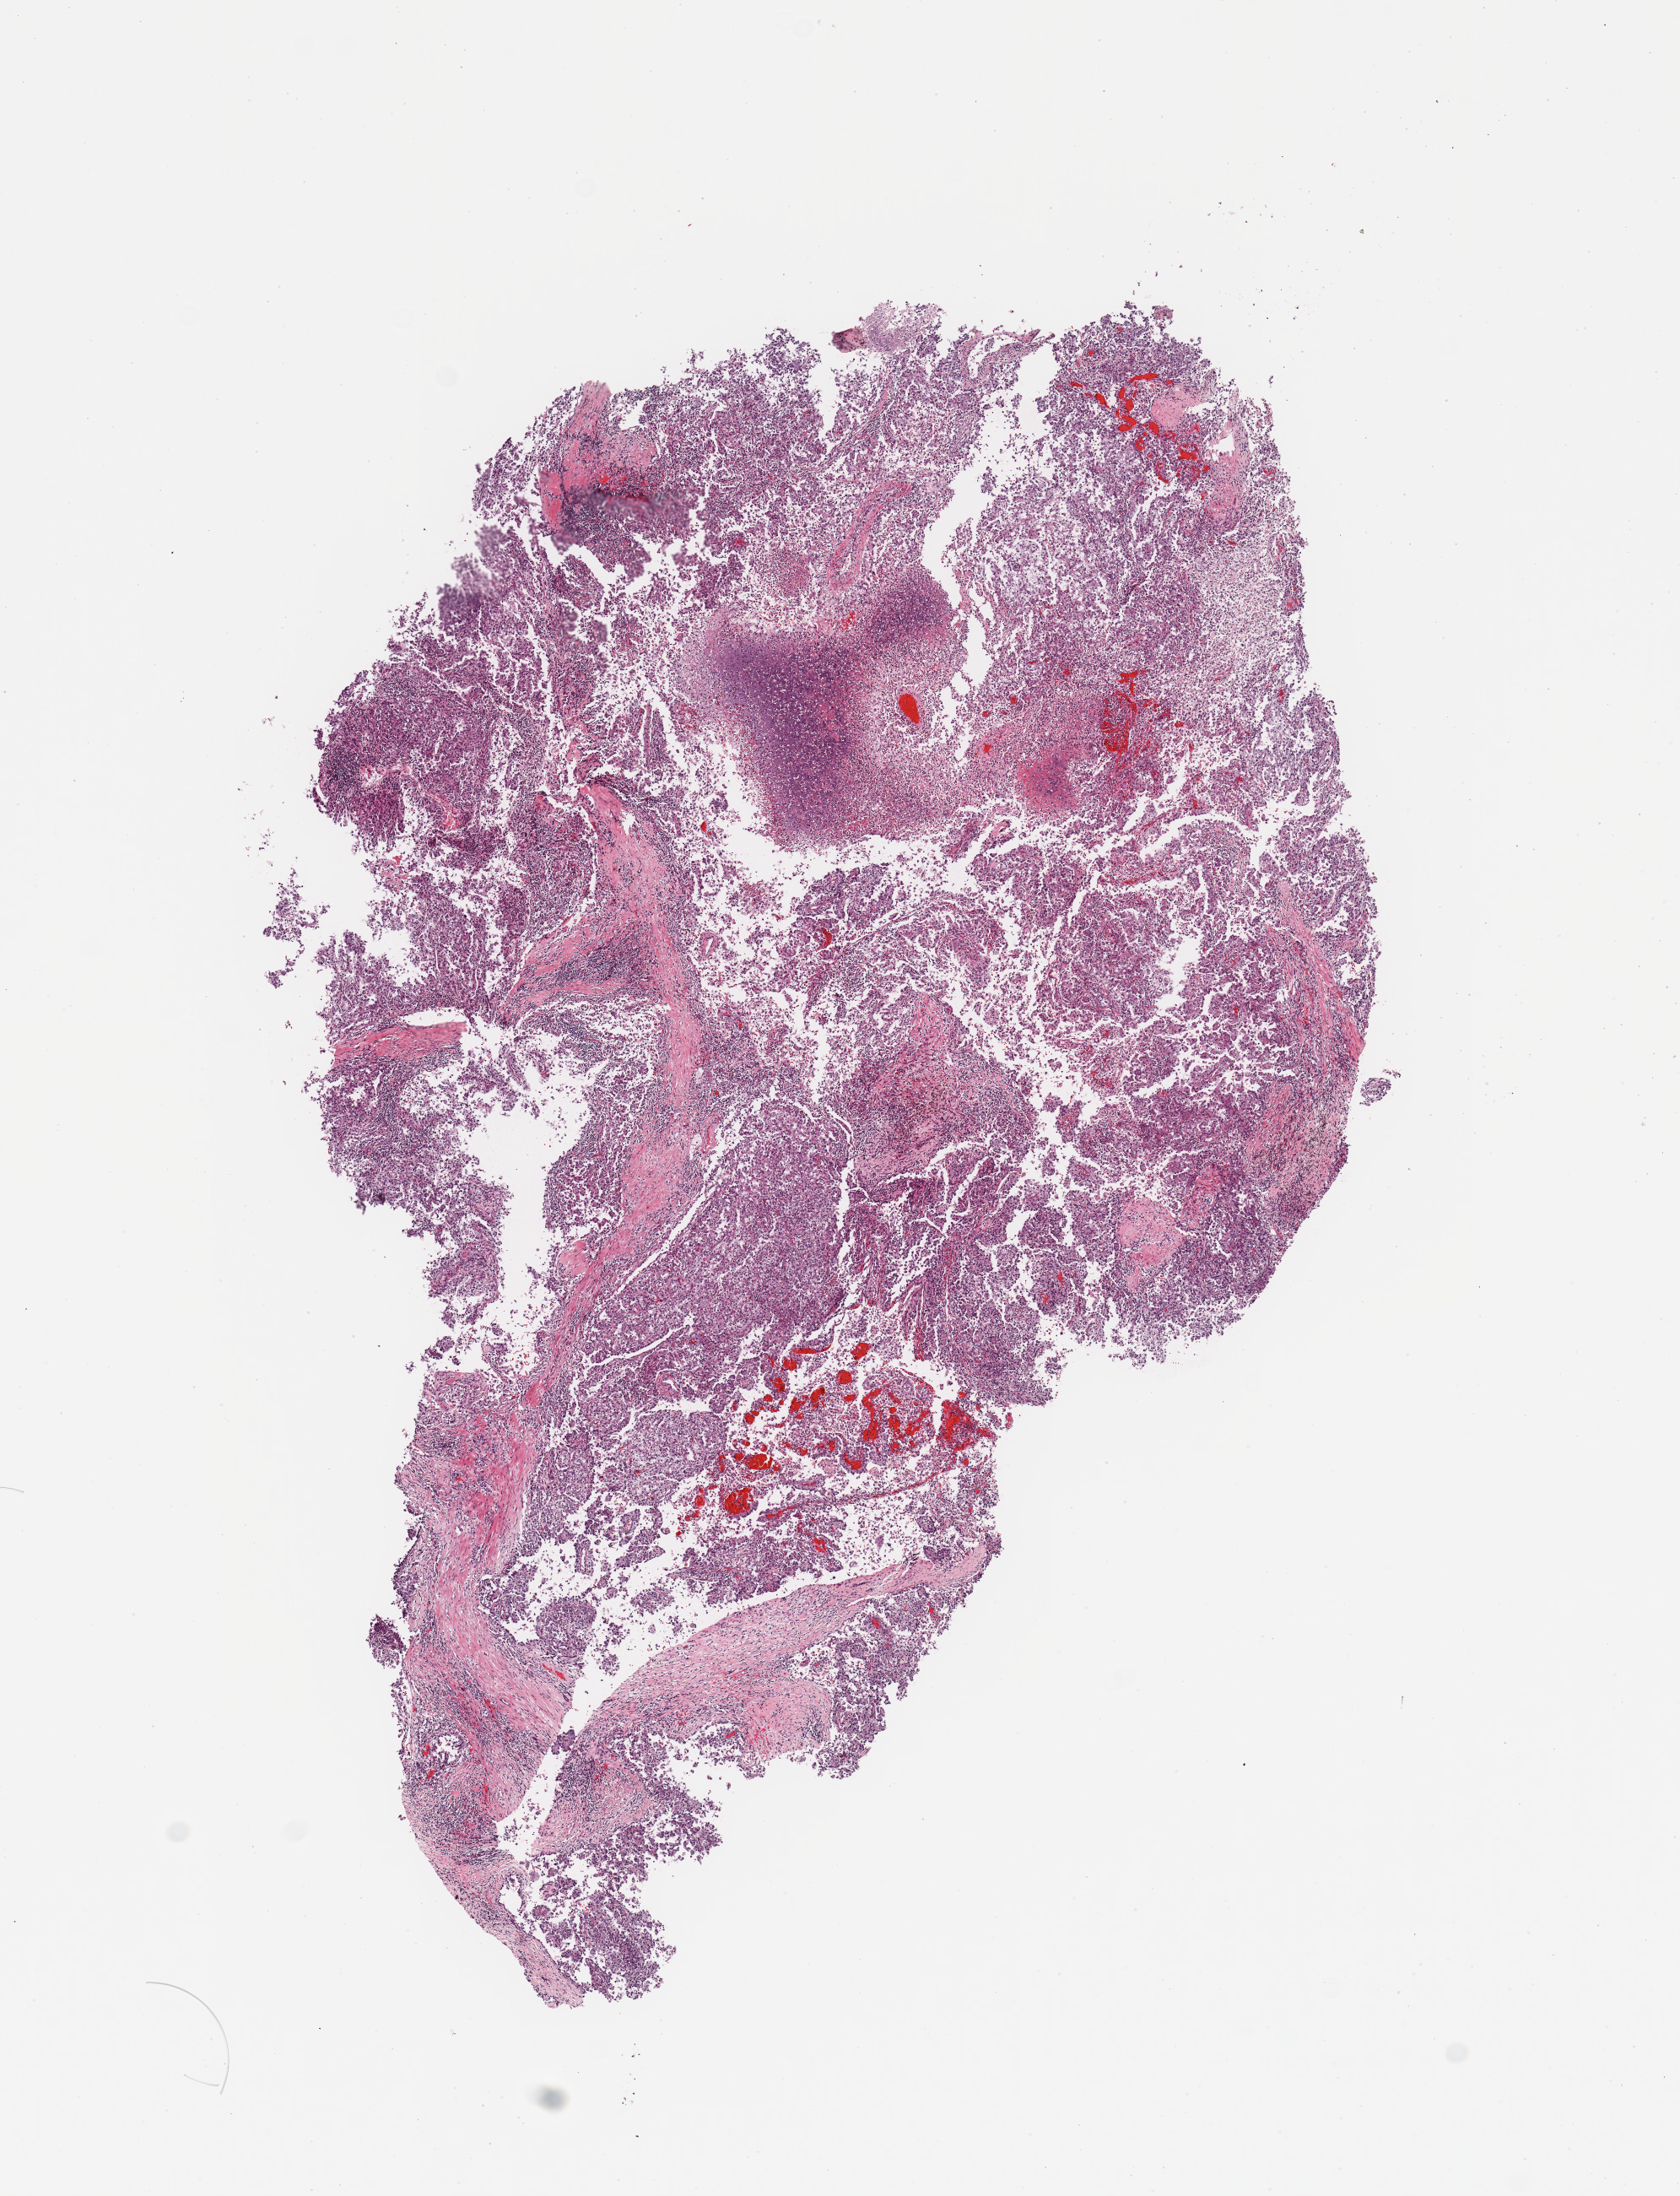
H&E-stained whole-slide image — whole scanned area (about 7.9 x 10.3 mm, from a 20x scan) shown as a low-resolution overview, tumour tissue sample, kidney. 50-year-old male patient.
Diagnosis: Renal cell carcinoma, NOS.